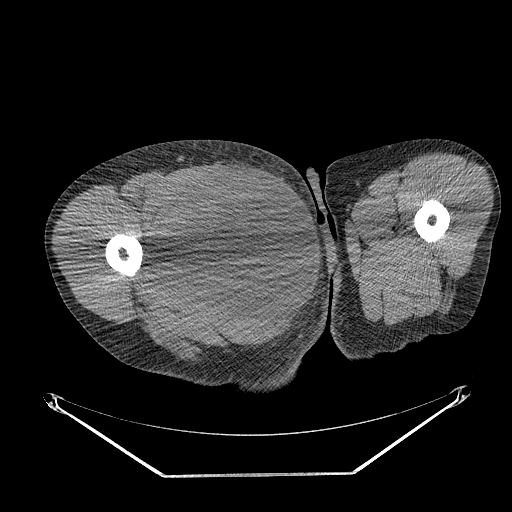
CT of an extremity soft-tissue mass (from a PET/CT study), one axial slice; position 266 of 311 along the scan axis; reconstruction kernel STANDARD; 140 kVp; soft-tissue window (W 400 / L 40 HU); 512 × 512 image matrix, field of view 500 × 500 mm. Male patient. From the clinical record (not read from this slice): histological type: undifferentiated - pleiomorphic; grade: high; site of the primary tumour: right thigh.
Outlined on this slice (expert contour drawn on MRI and transferred to this co-registered scan by the dataset authors):
- gross tumour volume including surrounding oedema: box from (x=155, y=169) to (x=268, y=280) px
- gross tumour volume (mass): (x=158, y=169)–(x=268, y=279)